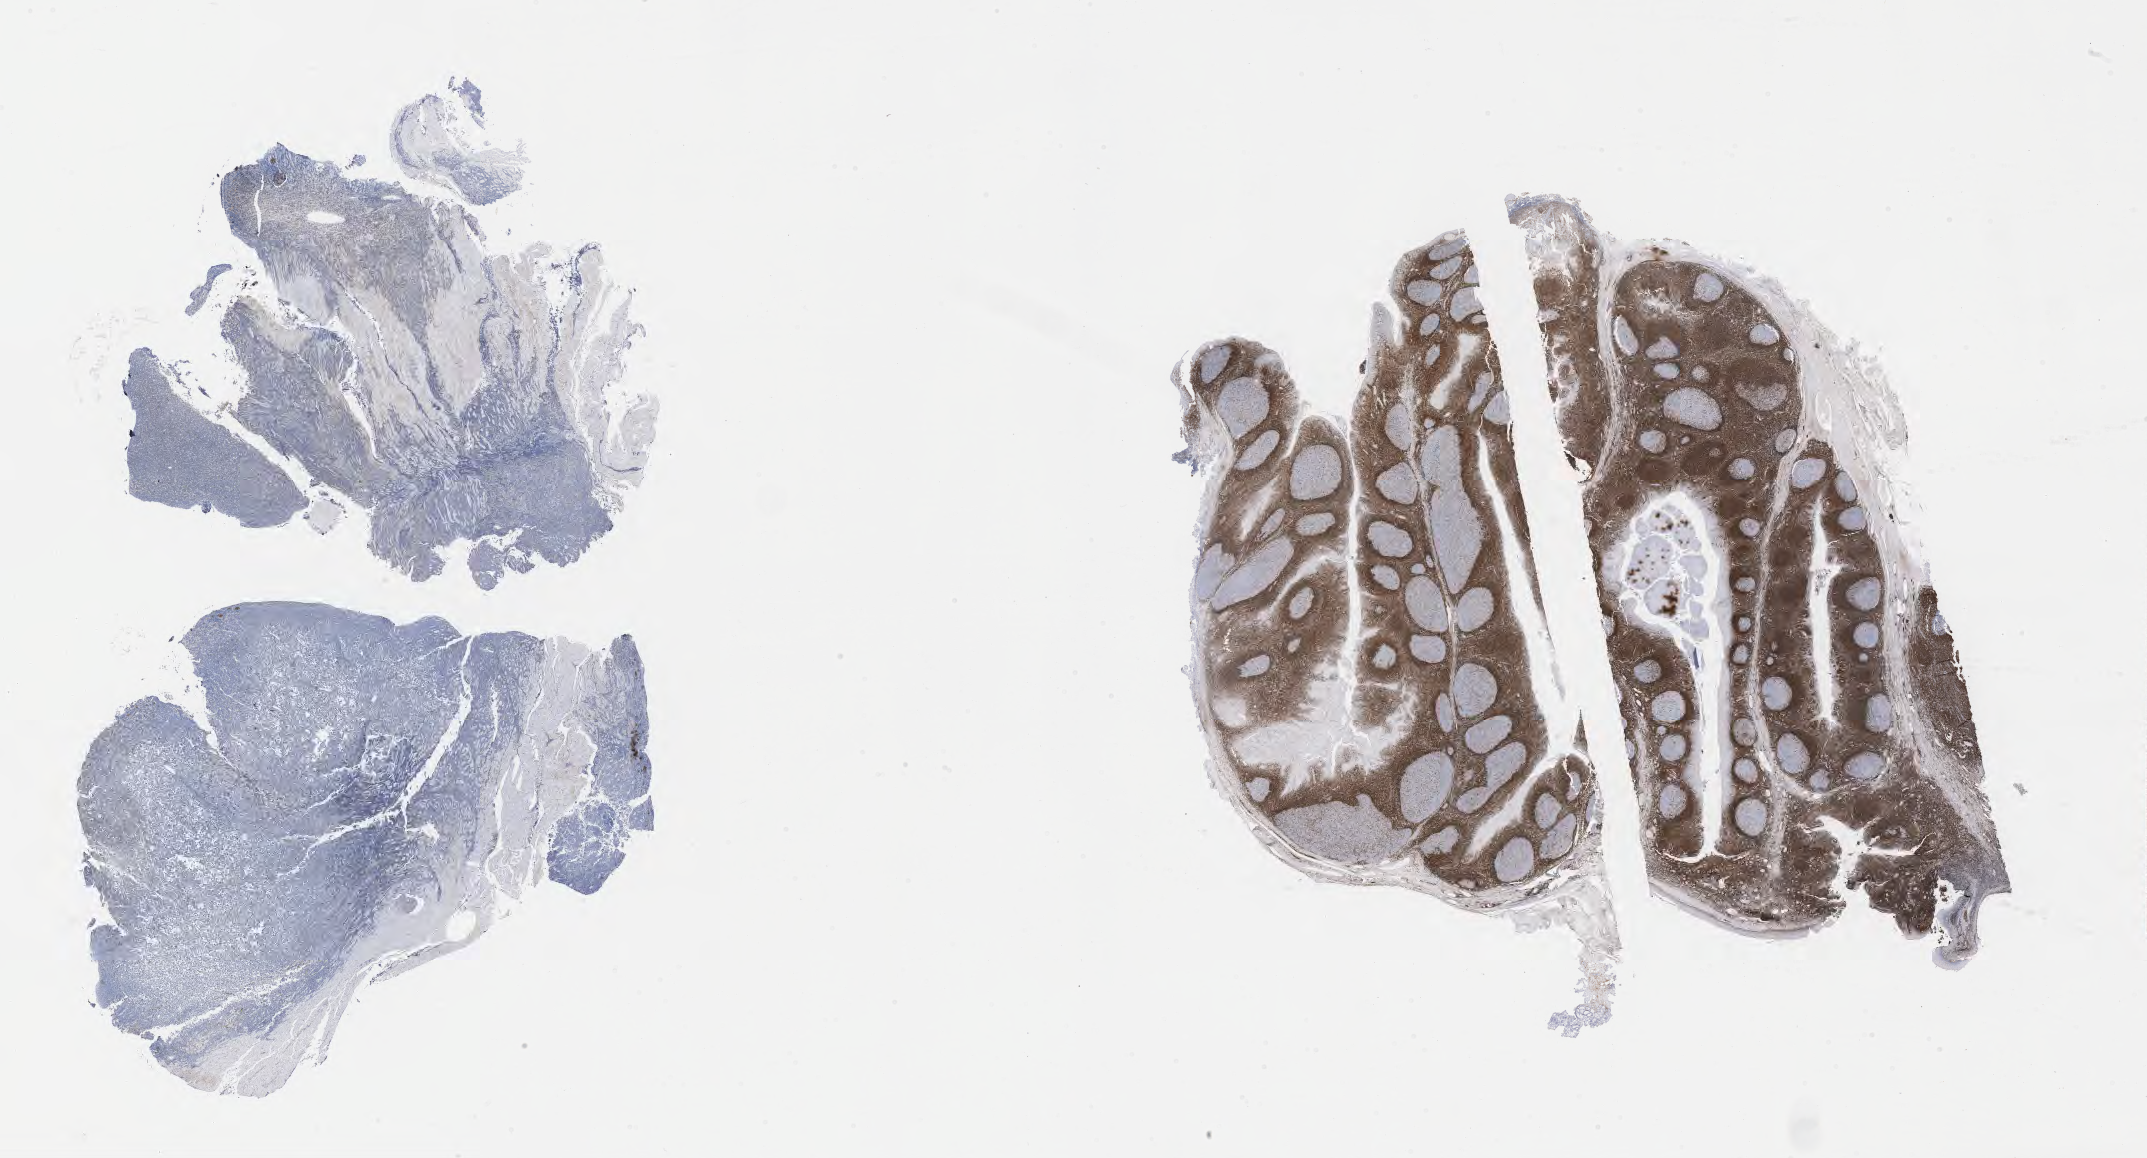
Whole-slide image, immunohistochemical stain for BCL2, whole scanned area (about 34.7 x 18.7 mm) shown as a low-resolution overview, specimen: tumor tissue. Patient: male, age 40 years.
Diagnosis: Burkitt lymphoma, NOS.